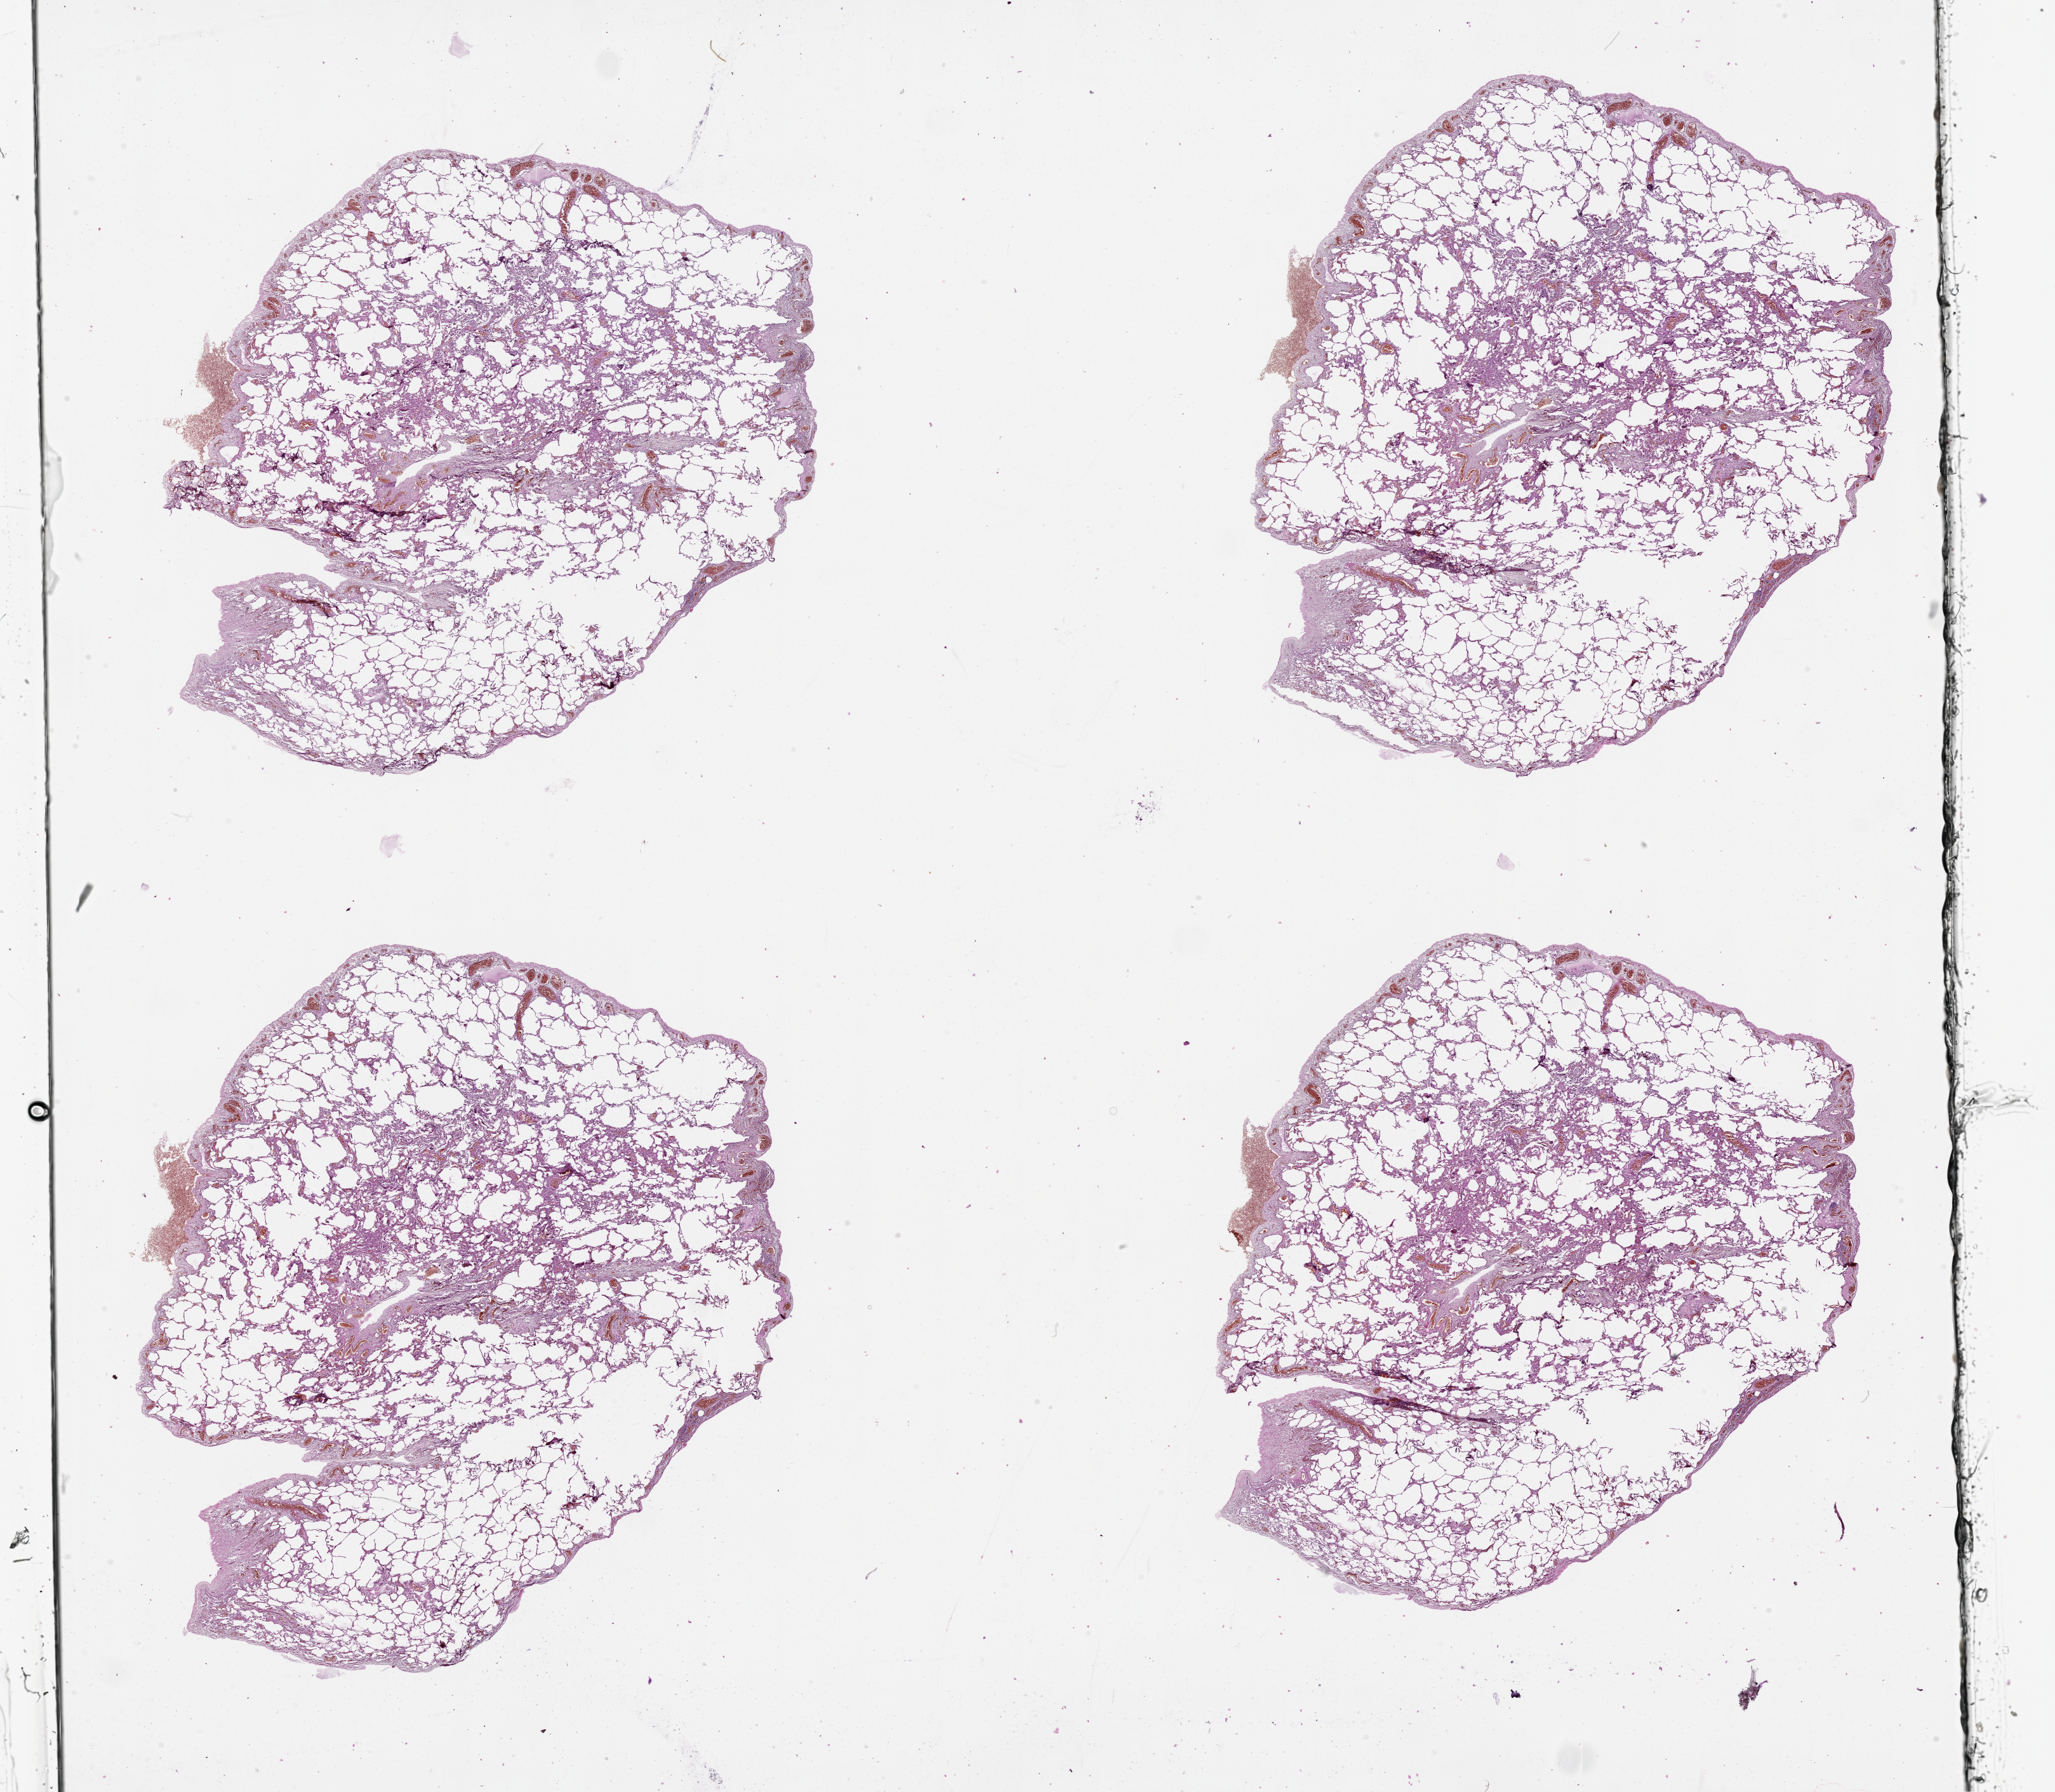
H&E whole-slide image, whole scanned area (about 26.1 x 22.7 mm, from a 20x scan) shown as a low-resolution overview, normal (non-tumour) tissue sample, sampled site: lung. 51-year-old female patient.
This section: normal (non-tumour) tissue from the same patient. Patient diagnosis: Adenocarcinoma, NOS.